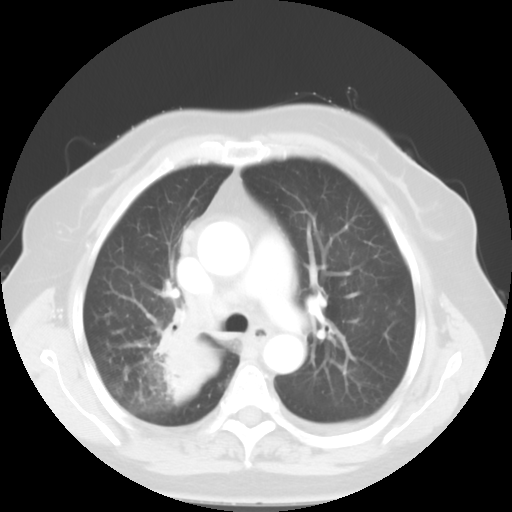
Chest CT, one axial slice. Position 35 of 52 along the scan axis. 120 kVp. Lung window (W 1500 / L -600 HU). 512 × 512 image matrix, field of view 333 × 333 mm. Patient: female, 81 years. Case-level facts recorded for this patient, not image findings: clinical TNM (as recorded): T4 N3 M1b.
Structures marked on this image (rectangle marked by the reading radiologist):
- lung tumour (recorded histology: adenocarcinoma): box from (x=154, y=305) to (x=219, y=406) px